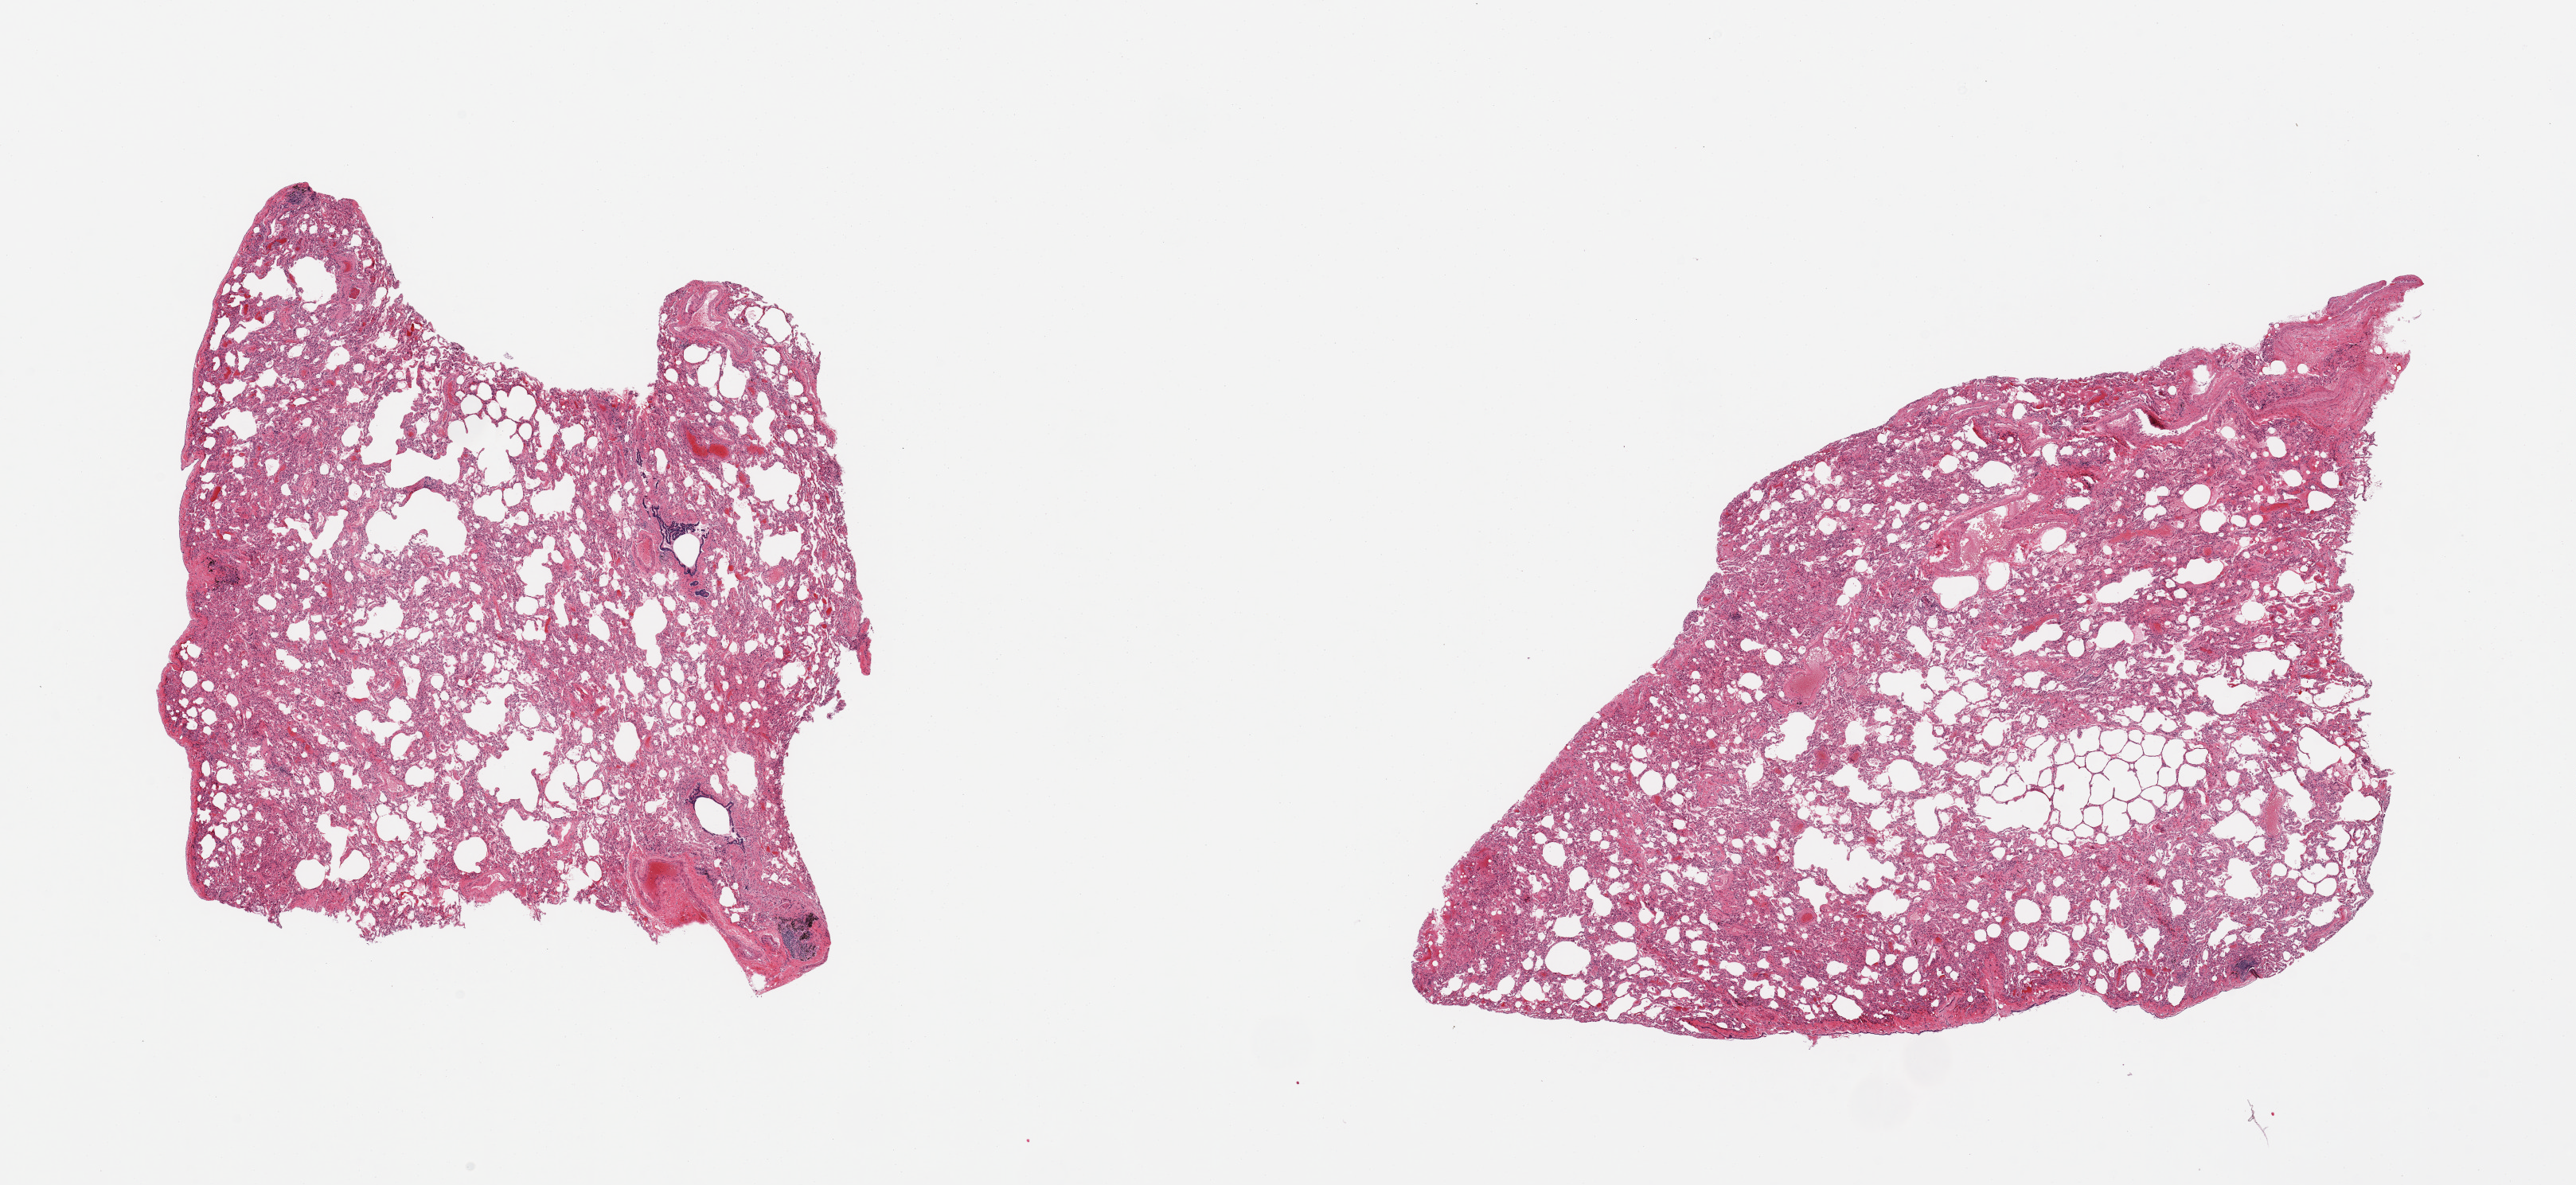
Digitized hematoxylin and eosin (H&E)-stained section, brightfield — a low-resolution overview of the entire scanned area, about 25.6 x 11.8 mm (from a 20x scan). PAXgene-fixed, paraffin-embedded tissue. Target tissue: lung. Donor tissue sample.
- pathologist's review note for this sample: 2 pieces; patchy emphysema; pleura sampled